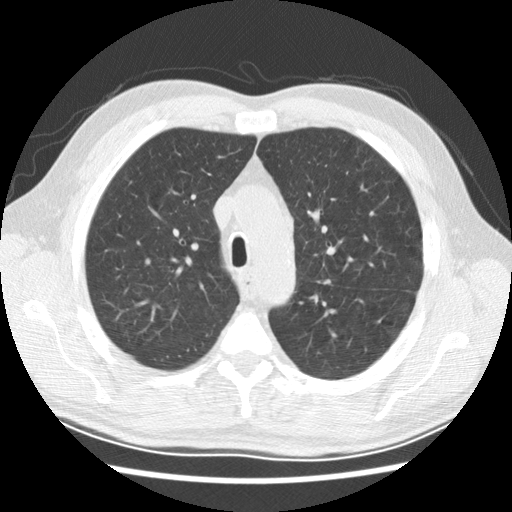
Low-dose screening chest CT, axial slice. Baseline annual screen. Lung window (W 1500 / L -600 HU). 2.5 mm slice thickness. Standard (soft-tissue) reconstruction kernel (STANDARD). Slice 63 of 236 in the series. 512 × 512 image matrix. Male, age 59 years at enrolment. Current smoker at enrolment.
Lesion marked by an expert reader, bounding box [x1, y1, x2, y2] px = [300, 269, 343, 295]. The exam's reader record, not a measurement of the box and not confirmed to be the same lesion: non-calcified nodule or mass ≥4 mm, left upper lobe, 8 × 5 mm, smooth margins, soft tissue attenuation. Official screen result: positive, change unspecified: nodule(s) >= 4 mm or enlarging nodule(s), mass(es), or other non-specific abnormalities suspicious for lung cancer.